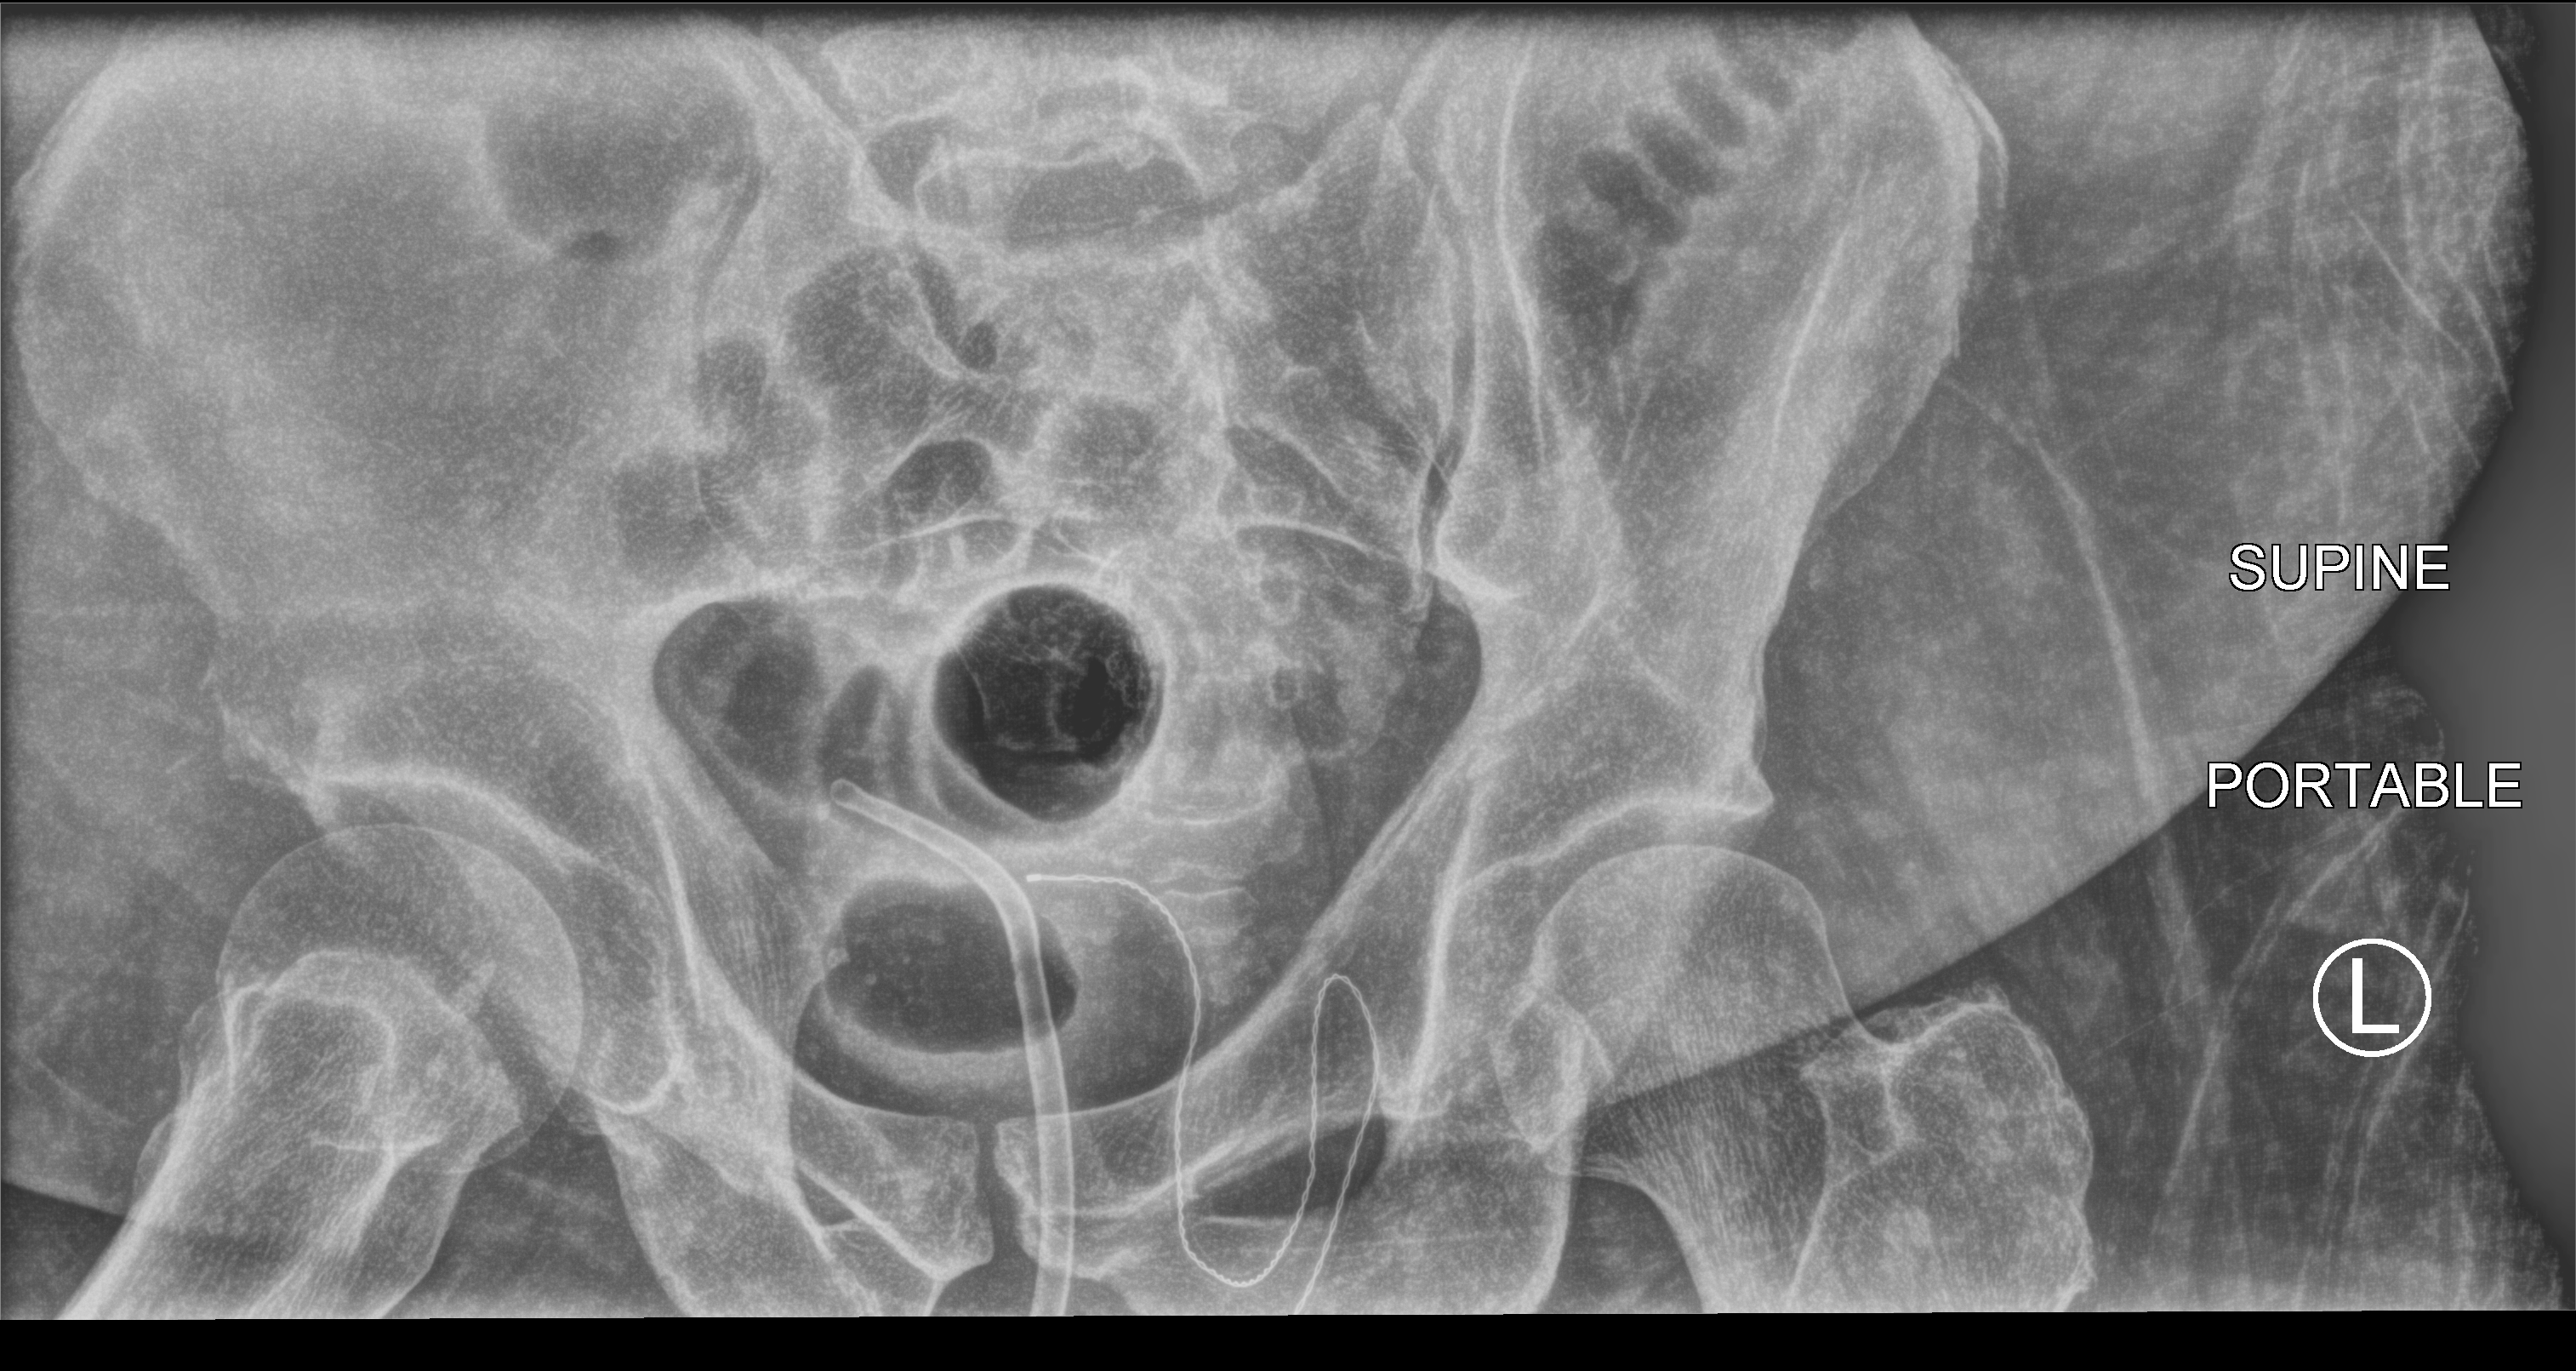
Abdomen X-ray (portable); anteroposterior (AP) projection. Patient hospitalised with COVID-19; male, aged 18–59 years.
Hospital-stay facts (about this admission, not read from this image; timing relative to this image not recorded):
- smoking status (admission record): never